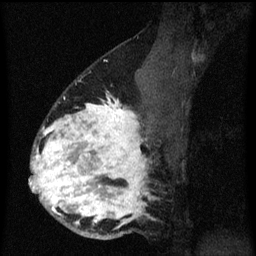
Breast MRI (dynamic contrast-enhanced), one sagittal slice; position 41 of 60 along the scan axis; dynamic contrast-enhanced series, image 2 of 3 at this slice position (ordered by acquisition); 1.5 T; TE 4.2 ms, TR 8.4 ms; 2 mm slice thickness; 256 × 256 image matrix, field of view 180 × 180 mm. Female patient, age 34 years. Case-level facts recorded for this patient, not image findings: setting: breast cancer imaged before/during neoadjuvant chemotherapy; receptor status: HR-positive, HER2-negative.
Outlined on this slice (semi-automatically segmented with operator editing):
- analysis volume of interest (the breast-tissue region the enhancement analysis was run in; not a lesion): box from (x=30, y=62) to (x=171, y=241) px
- tumour enhancement mask (voxels above the 70 % enhancement threshold inside the analysis volume of interest): (x=30, y=96)–(x=149, y=229)